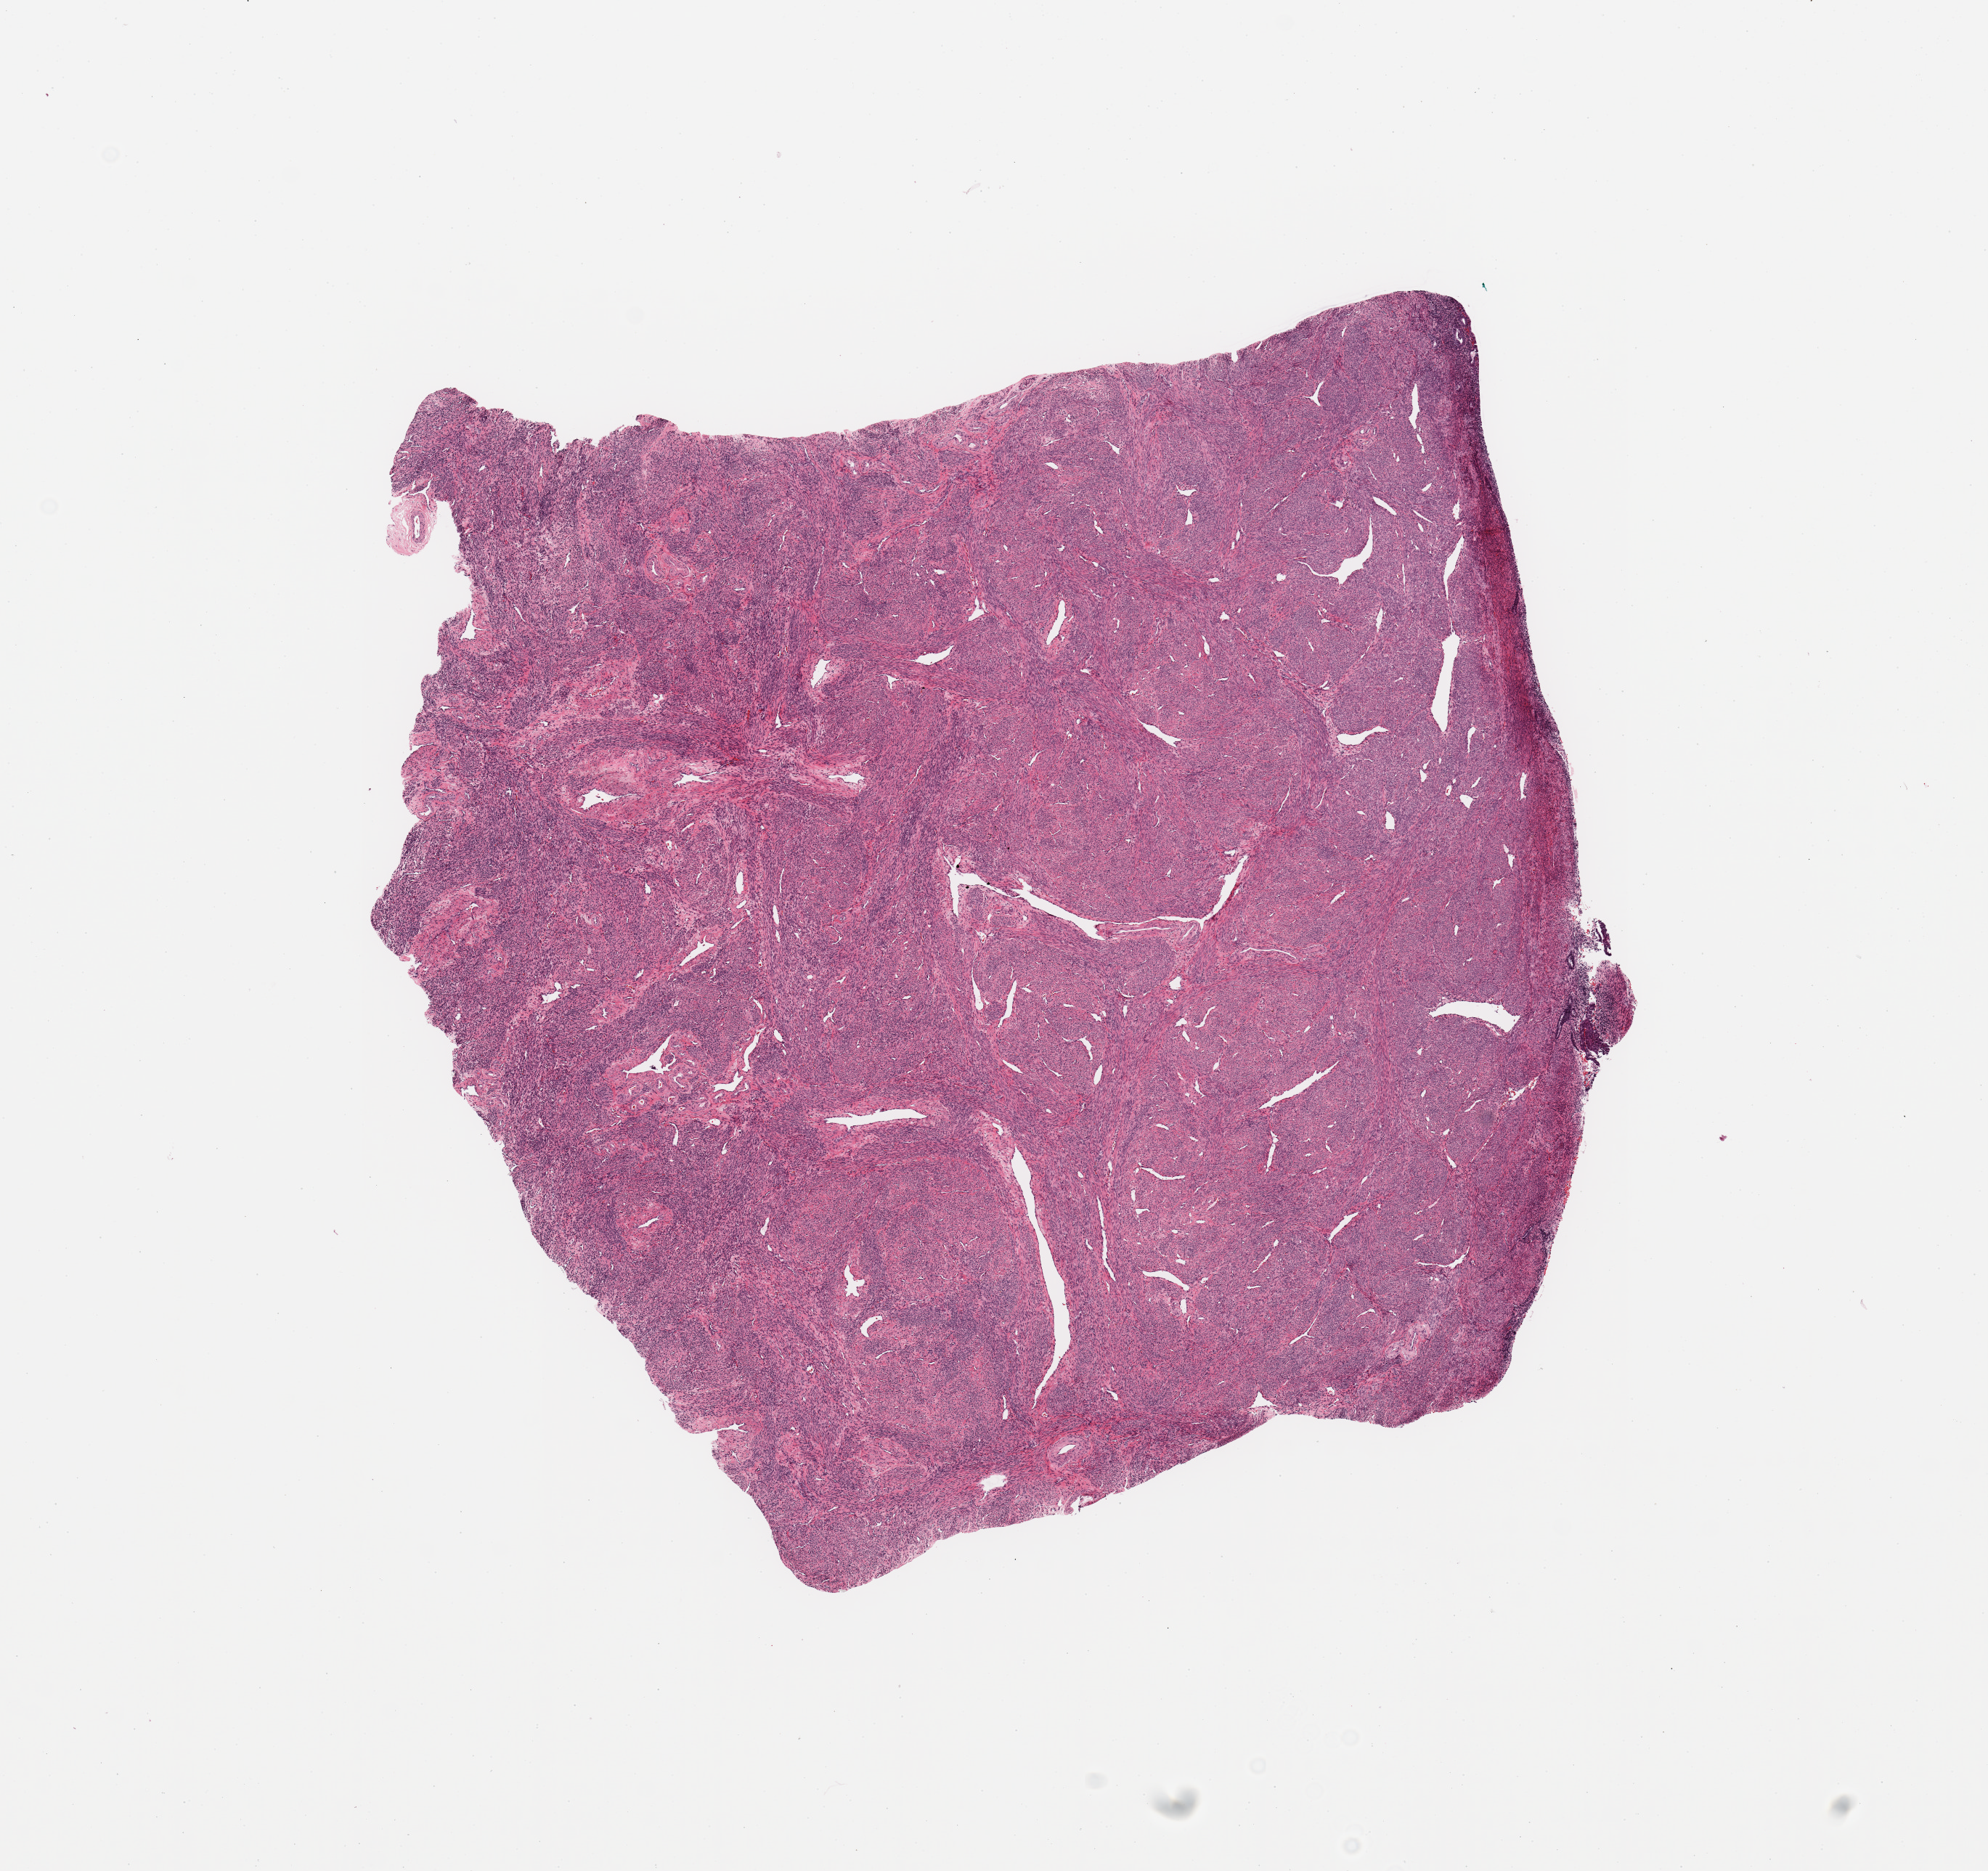
Whole-slide histology image, H&E — whole scanned area (about 10.8 x 10.2 mm, acquisition: 20x scan) shown as a low-resolution overview. Normal (non-tumour) tissue sample, sampled site: uterus. Female, 57 y/o.
This section: normal (non-tumour) tissue from the same patient. Patient diagnosis: Endometrioid adenocarcinoma, NOS.